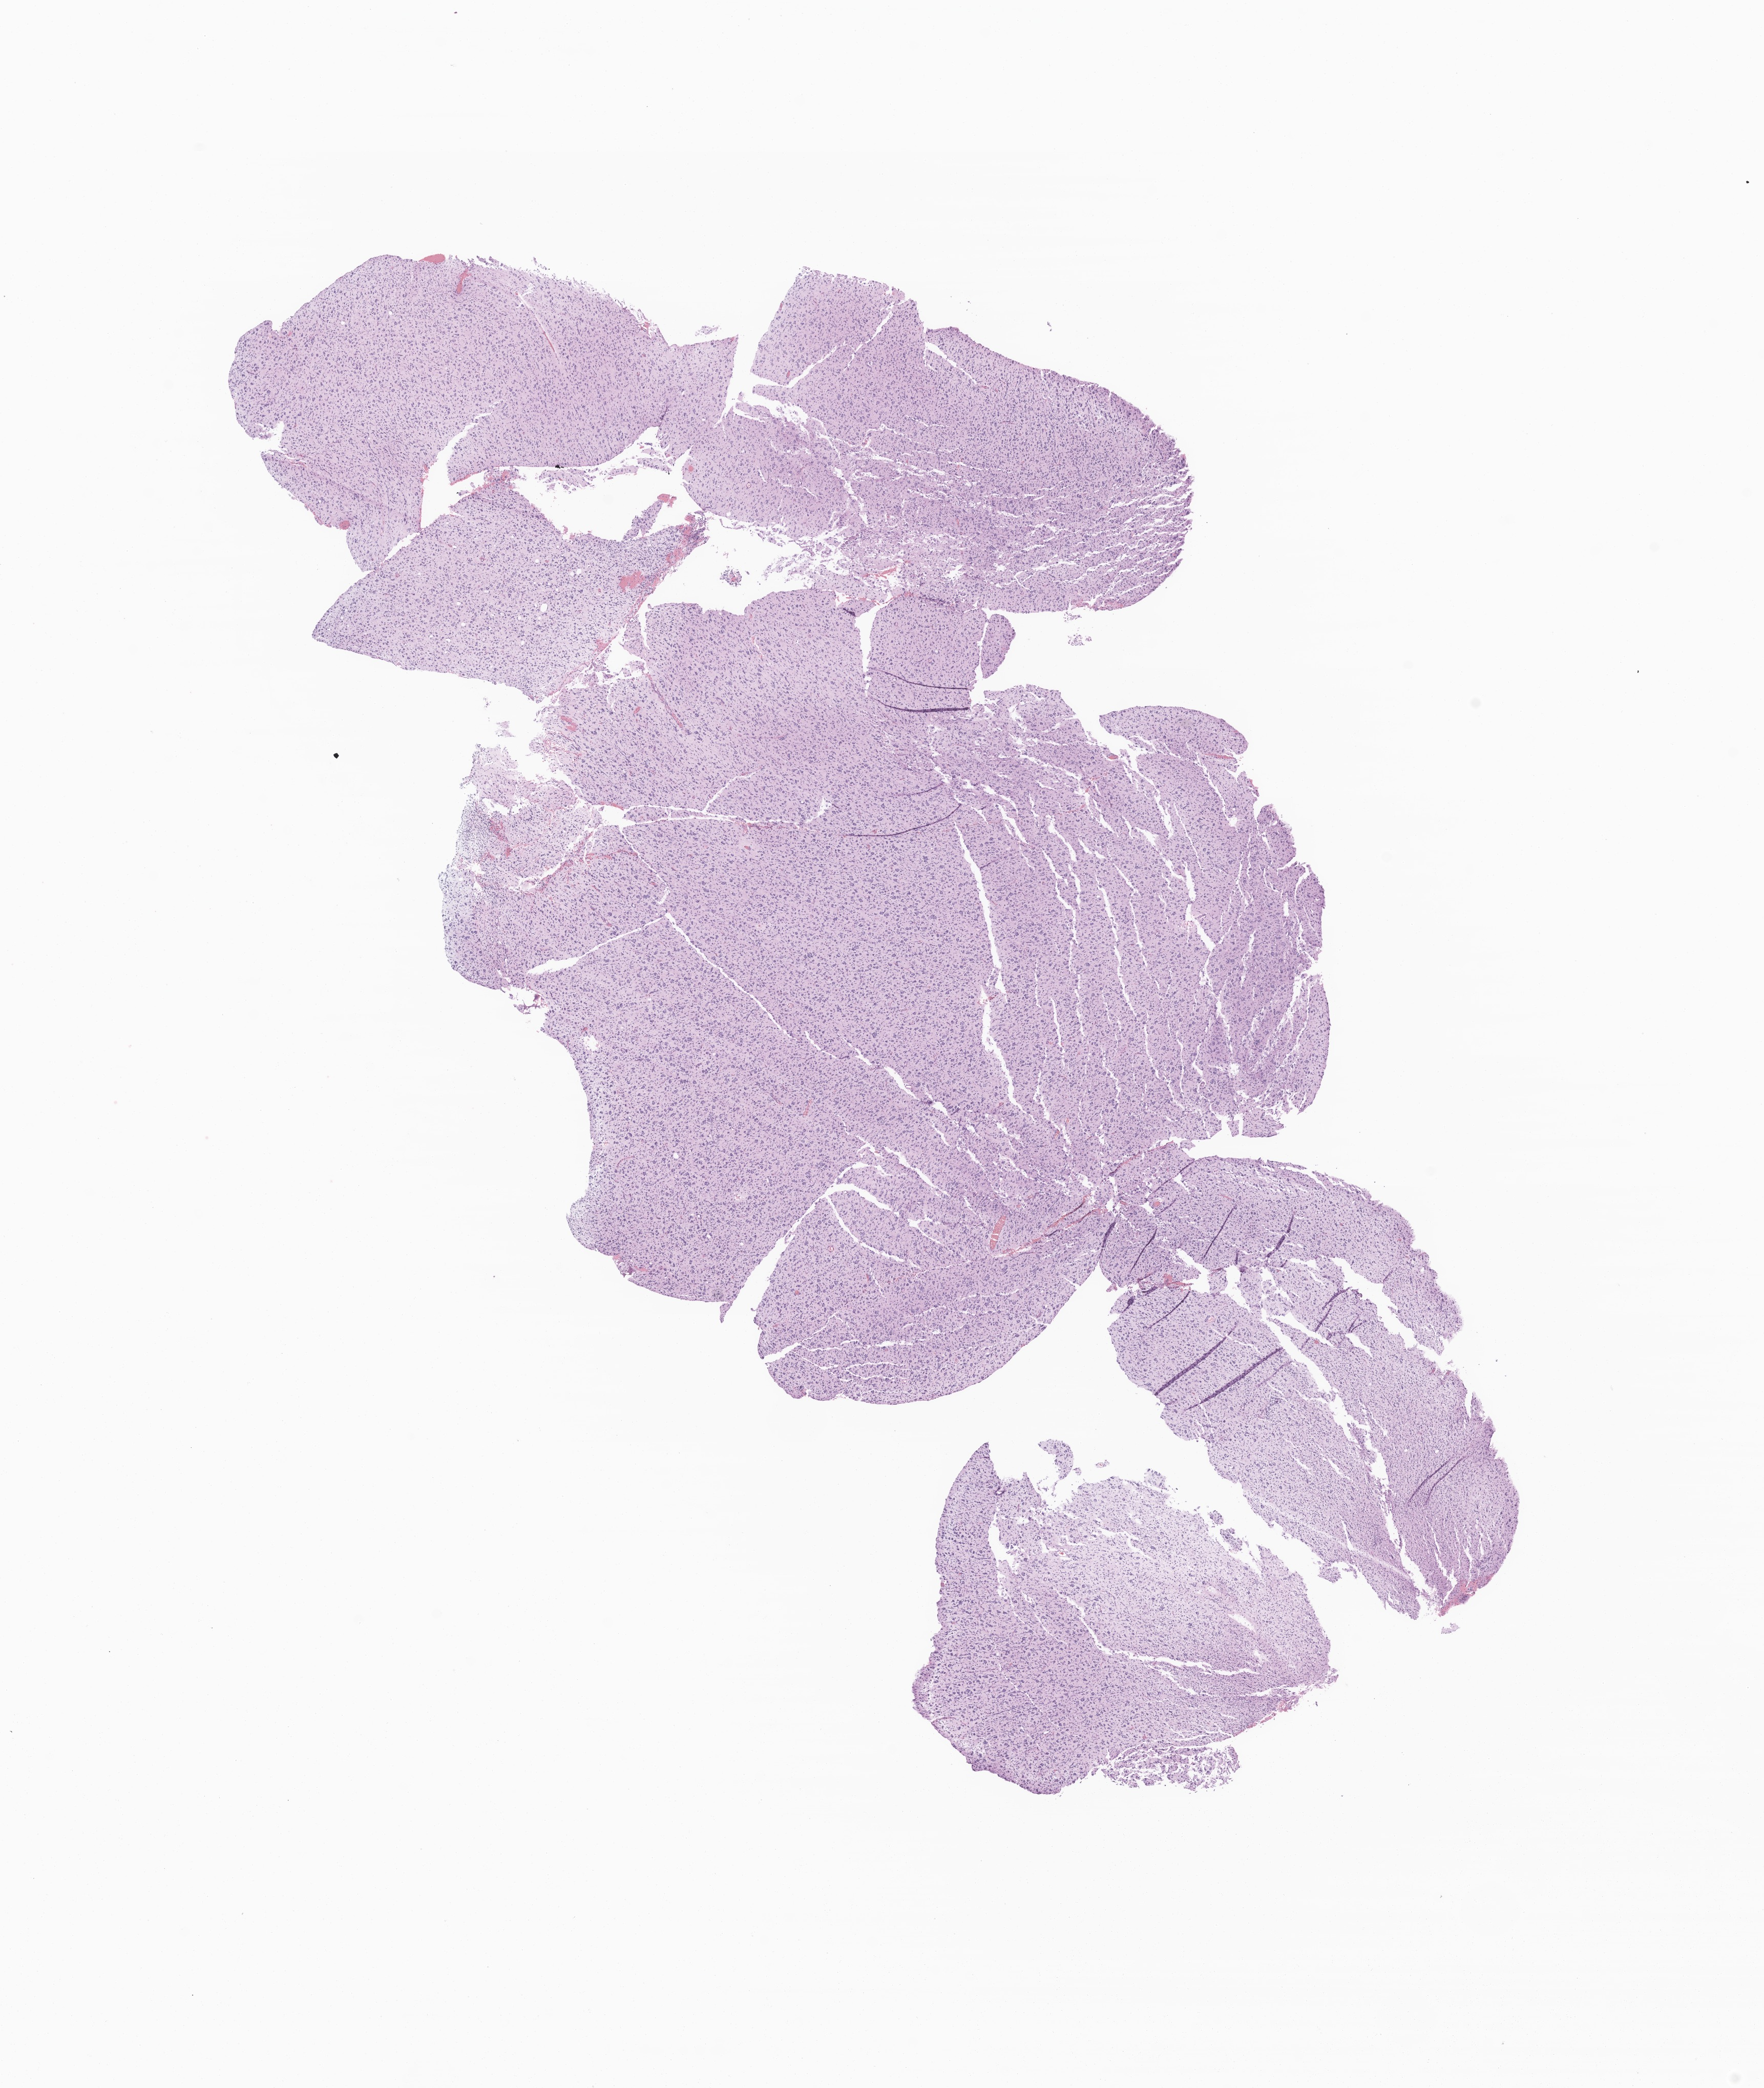
Haematoxylin and eosin whole-slide image of tumor tissue from the temporal lobe — whole scanned area (about 14.4 x 17.1 mm) shown as a low-resolution overview; formalin-fixed, paraffin-embedded (FFPE) tissue. Female patient, age 65 months (5 years 5 months).
• recorded diagnosis: Glioma, malignant